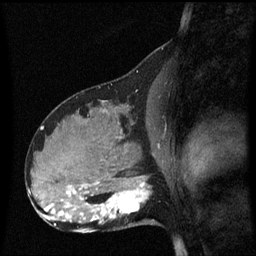
Breast MRI (dynamic contrast-enhanced), one sagittal slice; slice 30 of 60 in the series (ordered by position); dynamic contrast-enhanced series, image 2 of 3 at this slice position (ordered by acquisition); 1.5 T; TE 4.2 ms, TR 8.4 ms; 256 × 256 image matrix, field of view 210 × 210 mm. Patient: female, 31 years. Case-level facts recorded for this patient, not image findings: setting: breast cancer imaged before/during neoadjuvant chemotherapy; receptor status: HR-positive, HER2-negative.
Outlined on this slice (semi-automatic segmentation, software-assisted and operator-edited):
- analysis volume of interest (the breast-tissue region the enhancement analysis was run in; not a lesion): bounding box (x1, y1, x2, y2) in pixels: (98, 175, 156, 228)
- tumour enhancement mask (voxels above the 70 % enhancement threshold inside the analysis volume of interest): (99, 183, 149, 223)